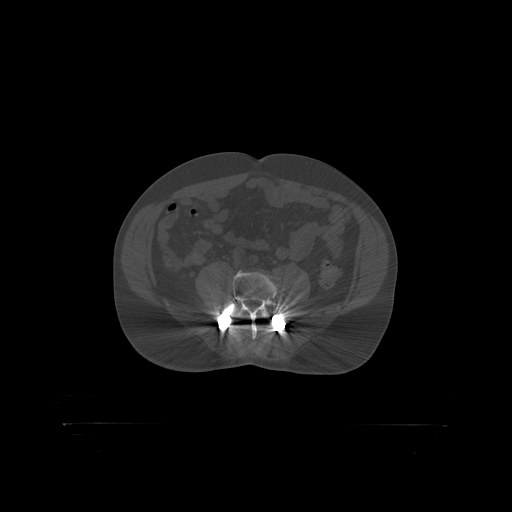
CT including the spine, one axial slice; position 215 of 399 along the scan axis; reconstruction kernel STANDARD; bone window (W 1800 / L 400 HU); 1.25 mm slice thickness; 512 × 512 image matrix, field of view 650 × 650 mm. Patient: male, 46 years. Case-level facts recorded for this patient, not image findings: primary cancer: skin.
Structures marked on this image (semi-automatically segmented with operator editing):
- L4 vertebra: box from (x=235, y=313) to (x=270, y=318) px
- L5 vertebra: (x=217, y=273)–(x=290, y=319)